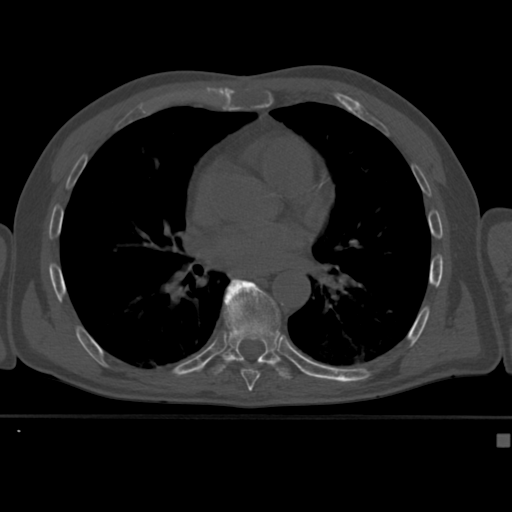
CT including the spine, one axial slice. Slice 254 of 430 in the series (ordered by position). Reconstruction kernel Br40s. 120 kVp. Bone window (W 1800 / L 400 HU). 1.5 mm slice thickness. 512 × 512 image matrix, field of view 337 × 337 mm. Male patient, age 64 years. Case-level facts recorded for this patient, not image findings: primary cancer: uterus; vertebrae with lytic lesions (as recorded): T1, T4, T5, T7, L5.
Structures marked on this image (semi-automatic segmentation, software-assisted and operator-edited):
- T8 vertebra: box from (x=224, y=332) to (x=261, y=382) px
- T9 vertebra: (x=208, y=278)–(x=292, y=380)